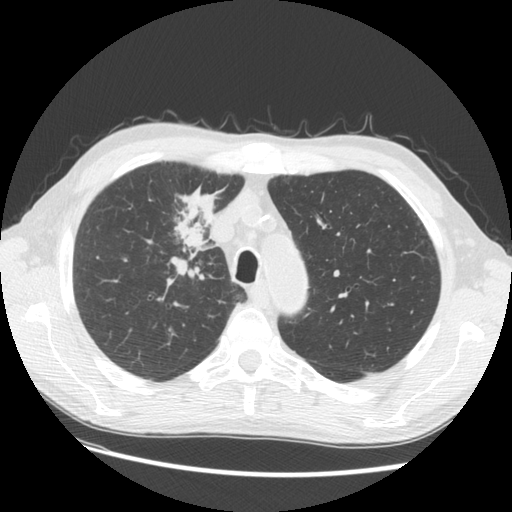
Low-dose screening chest CT, one axial slice; position 103 of 133 along the scan axis; 120 kVp; lung window (W 1500 / L -600 HU); 2.5 mm slice thickness; 512 × 512 image matrix, field of view 360 × 360 mm.
Structures marked on this image (manually delineated by an expert):
- lesion 1 (tumor, hilum of right lung): bounding box (x1, y1, x2, y2) in pixels: (175, 183, 217, 261)